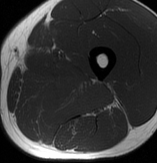
MRI of an extremity soft-tissue mass, one axial slice; position 37 of 70 along the scan axis; MR volume resampled by the dataset authors to the PET/CT grid (not the native acquisition matrix); 3.27 mm slice thickness; 157 × 163 image matrix, field of view 153 × 159 mm. Male patient. From the clinical record (not read from this slice): histological type: extraskeletal osteosarcoma; grade: high; site of the primary tumour: left adductur.
Annotated regions visible in this slice (expert contour drawn on MRI and transferred to this co-registered scan by the dataset authors):
- gross tumour volume (mass): bounding box <19,67,123,121> (left, top, right, bottom; pixels)